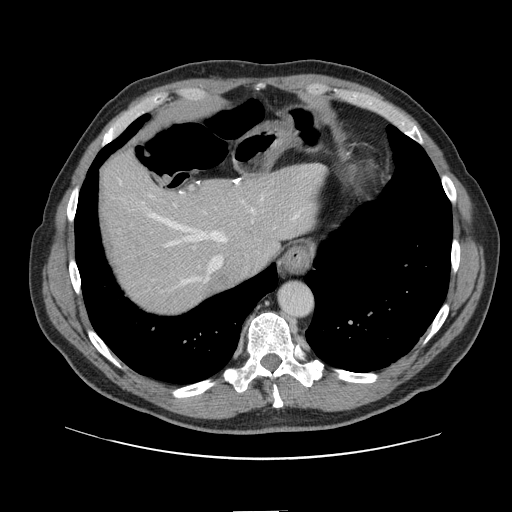
Contrast-enhanced abdominal CT, one axial slice. Position 120 of 161 along the scan axis. Intravenous contrast given. Soft-tissue window (W 400 / L 40 HU). 512 × 512 image matrix. Male patient, age 66 years. Case-level facts recorded for this patient, not image findings: diagnosis: colorectal cancer liver metastases, imaged before liver resection; multiple liver metastases: no; largest metastasis: 3.5 cm; chemotherapy before resection: yes.
Structures marked on this image (outlined manually by an expert reader):
- hepatic veins: bounding box <121,182,300,286> (left, top, right, bottom; pixels)
- liver: <100,156,321,313>
- planned liver remnant (the part of the liver to remain after resection): <100,154,320,299>
- liver metastasis: <205,272,227,294>